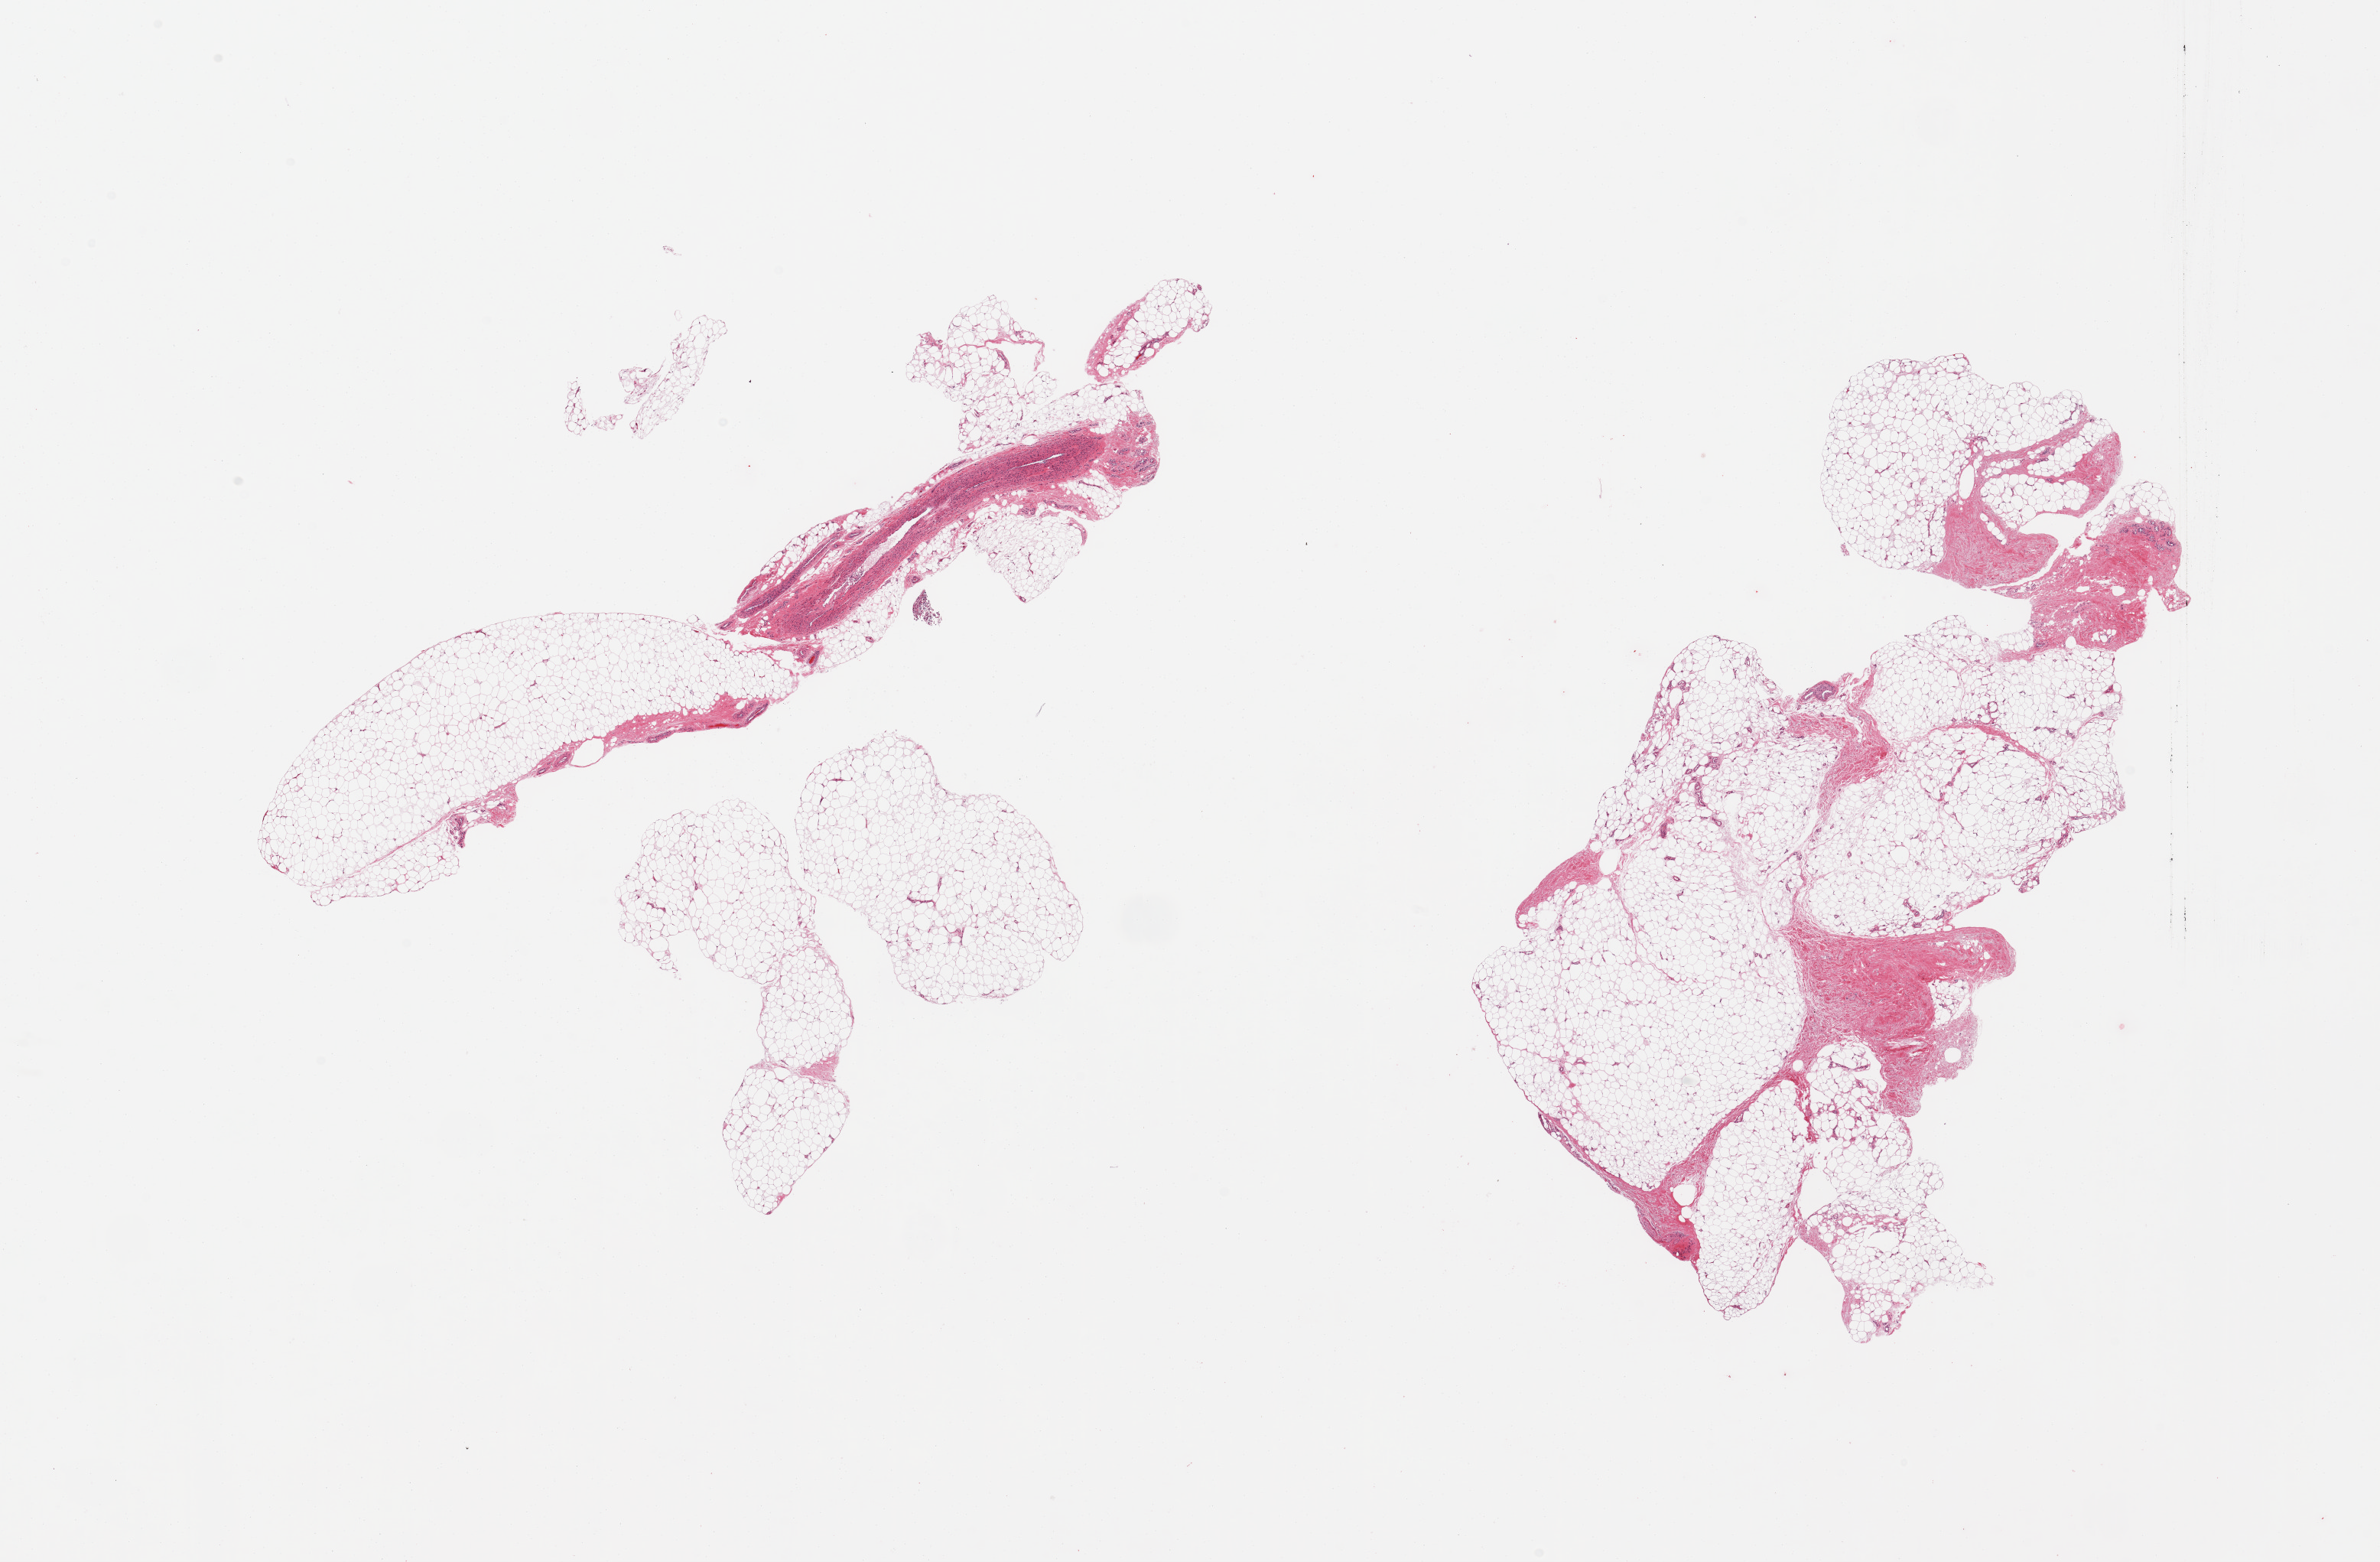
Digitized haematoxylin and eosin-stained section, brightfield — whole scanned area (about 24.6 x 16.1 mm) shown as a low-resolution overview. PAXgene-fixed, paraffin-embedded tissue. Sampled site (target tissue): adipose tissue. Donor tissue sample. Donor: male.
Review note (as recorded): 2 pieces, ~20% fascia/vascular elements.